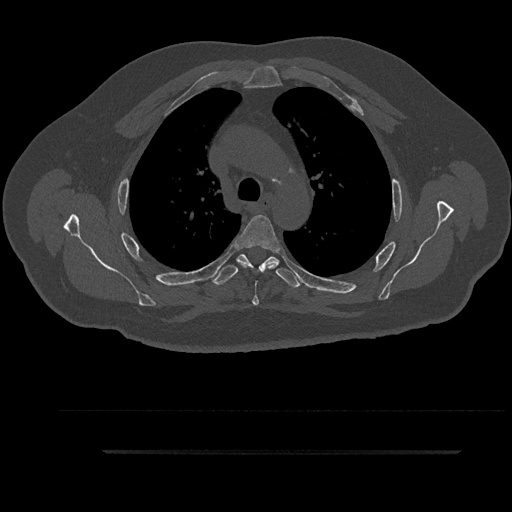
CT including the spine, one axial slice; slice 654 of 797 in the series (ordered by position); 120 kVp; bone window (W 1800 / L 400 HU); 512 × 512 image matrix, field of view 432 × 432 mm. Patient: male, 63 years. Case-level facts recorded for this patient, not image findings: primary cancer: renal; vertebrae with lytic lesions (as recorded): T8.
Structures marked on this image (semi-automatic segmentation, software-assisted and operator-edited):
- T3 vertebra: bounding box [x1, y1, x2, y2] px = [236, 259, 298, 278]
- T4 vertebra: [235, 215, 281, 306]
- T5 vertebra: [212, 254, 301, 289]